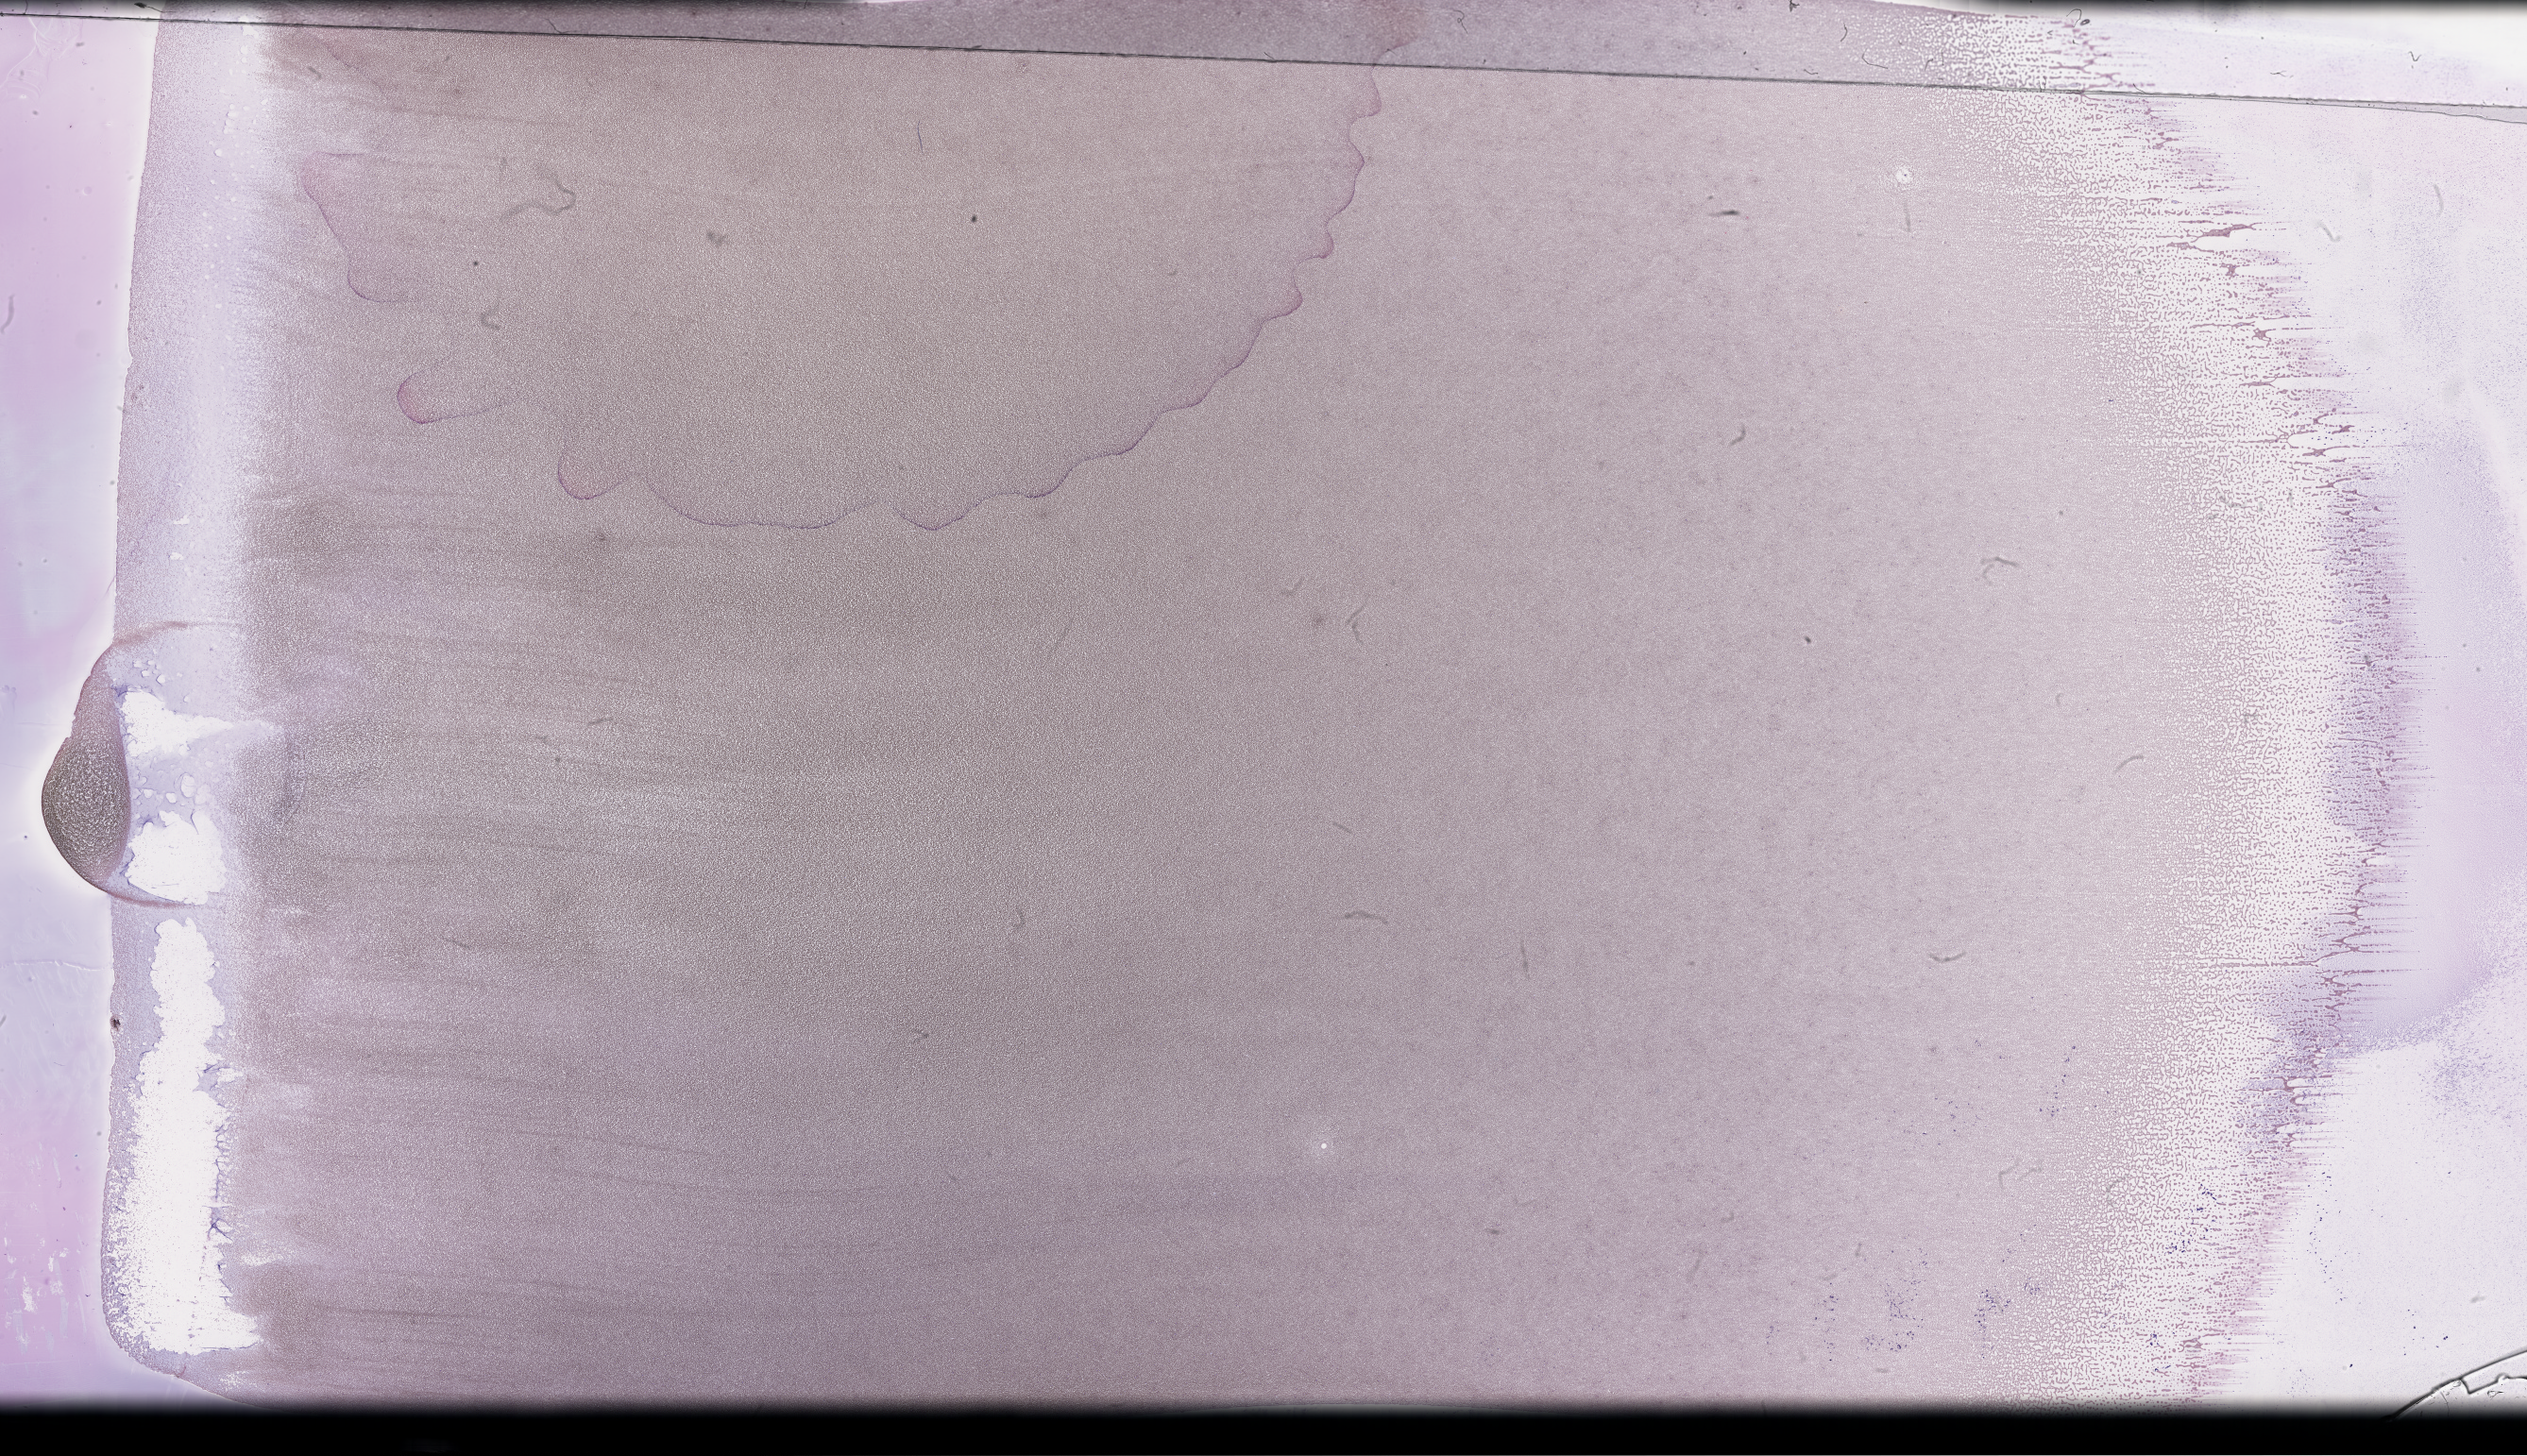
Wright-Giemsa-stained whole blood smear, whole-slide image, a low-resolution overview of the entire scanned area, about 43.2 x 24.9 mm; collected on treatment. Male patient.
* from a patient with: Plasma Cell Myeloma